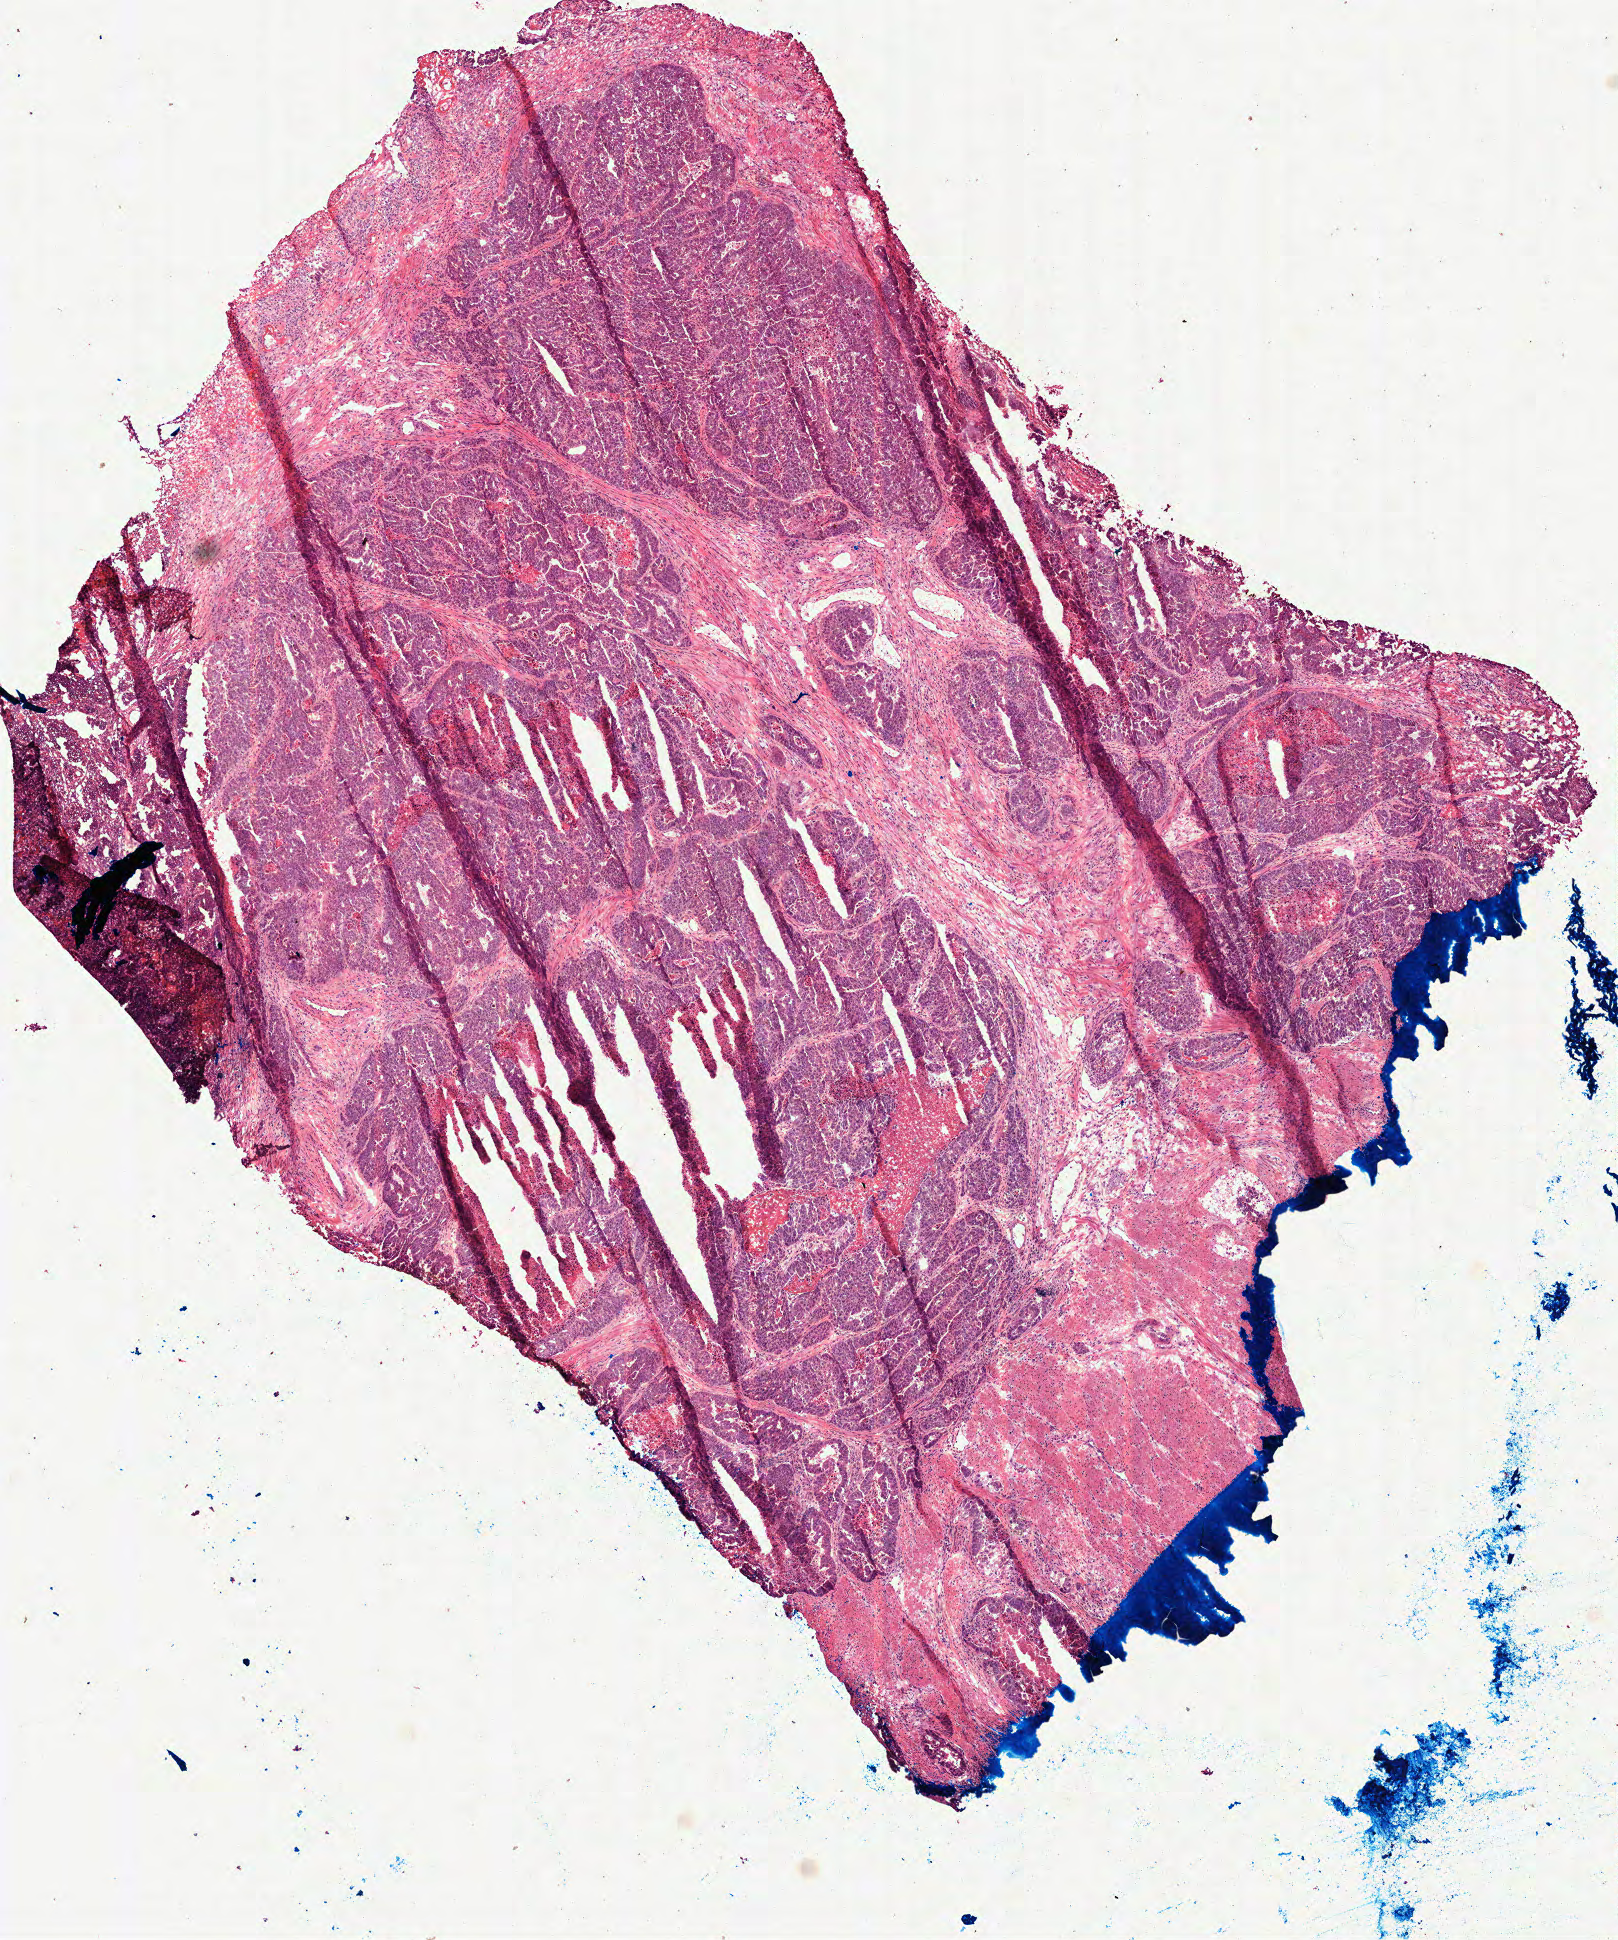
Digitized Hematoxylin and eosin (H&E) stained tissue section (whole slide), a low-resolution overview of the entire scanned area, about 6.5 x 7.8 mm, frozen section from the bottom of the tissue portion, sample: primary tumour, rectum. Male, age 50 years at initial diagnosis. Pathologist review of this section (percent, as recorded): tumour cells 70%, tumour nuclei 85%, normal cells 0%, stromal cells 15%, necrosis 15%.
Lymph nodes positive (case pathology): 8 of 15 examined. Histologic diagnosis: Adenocarcinoma, NOS (rectosigmoid junction). TNM: T3 N2b M0. AJCC pathologic stage: IIIC.